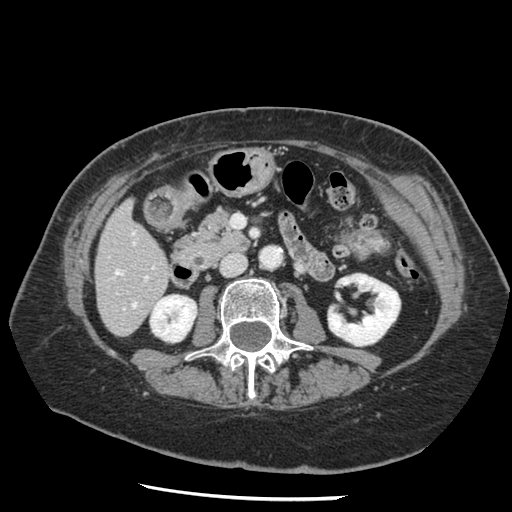
Contrast-enhanced abdominal CT, one axial slice. Position 46 of 148 along the scan axis. 120 kVp. Intravenous contrast given. Soft-tissue window (W 400 / L 40 HU). 2.5 mm slice thickness. 512 × 512 image matrix, field of view 330 × 330 mm. Female patient, age 85 years. From the clinical record (not read from this slice): diagnosis: colorectal cancer liver metastases, imaged before liver resection.
Structures marked on this image (expert manual segmentation):
- hepatic veins: bounding box <115,270,136,307> (left, top, right, bottom; pixels)
- liver: <96,203,170,336>
- planned liver remnant (the part of the liver to remain after resection): <96,203,170,333>